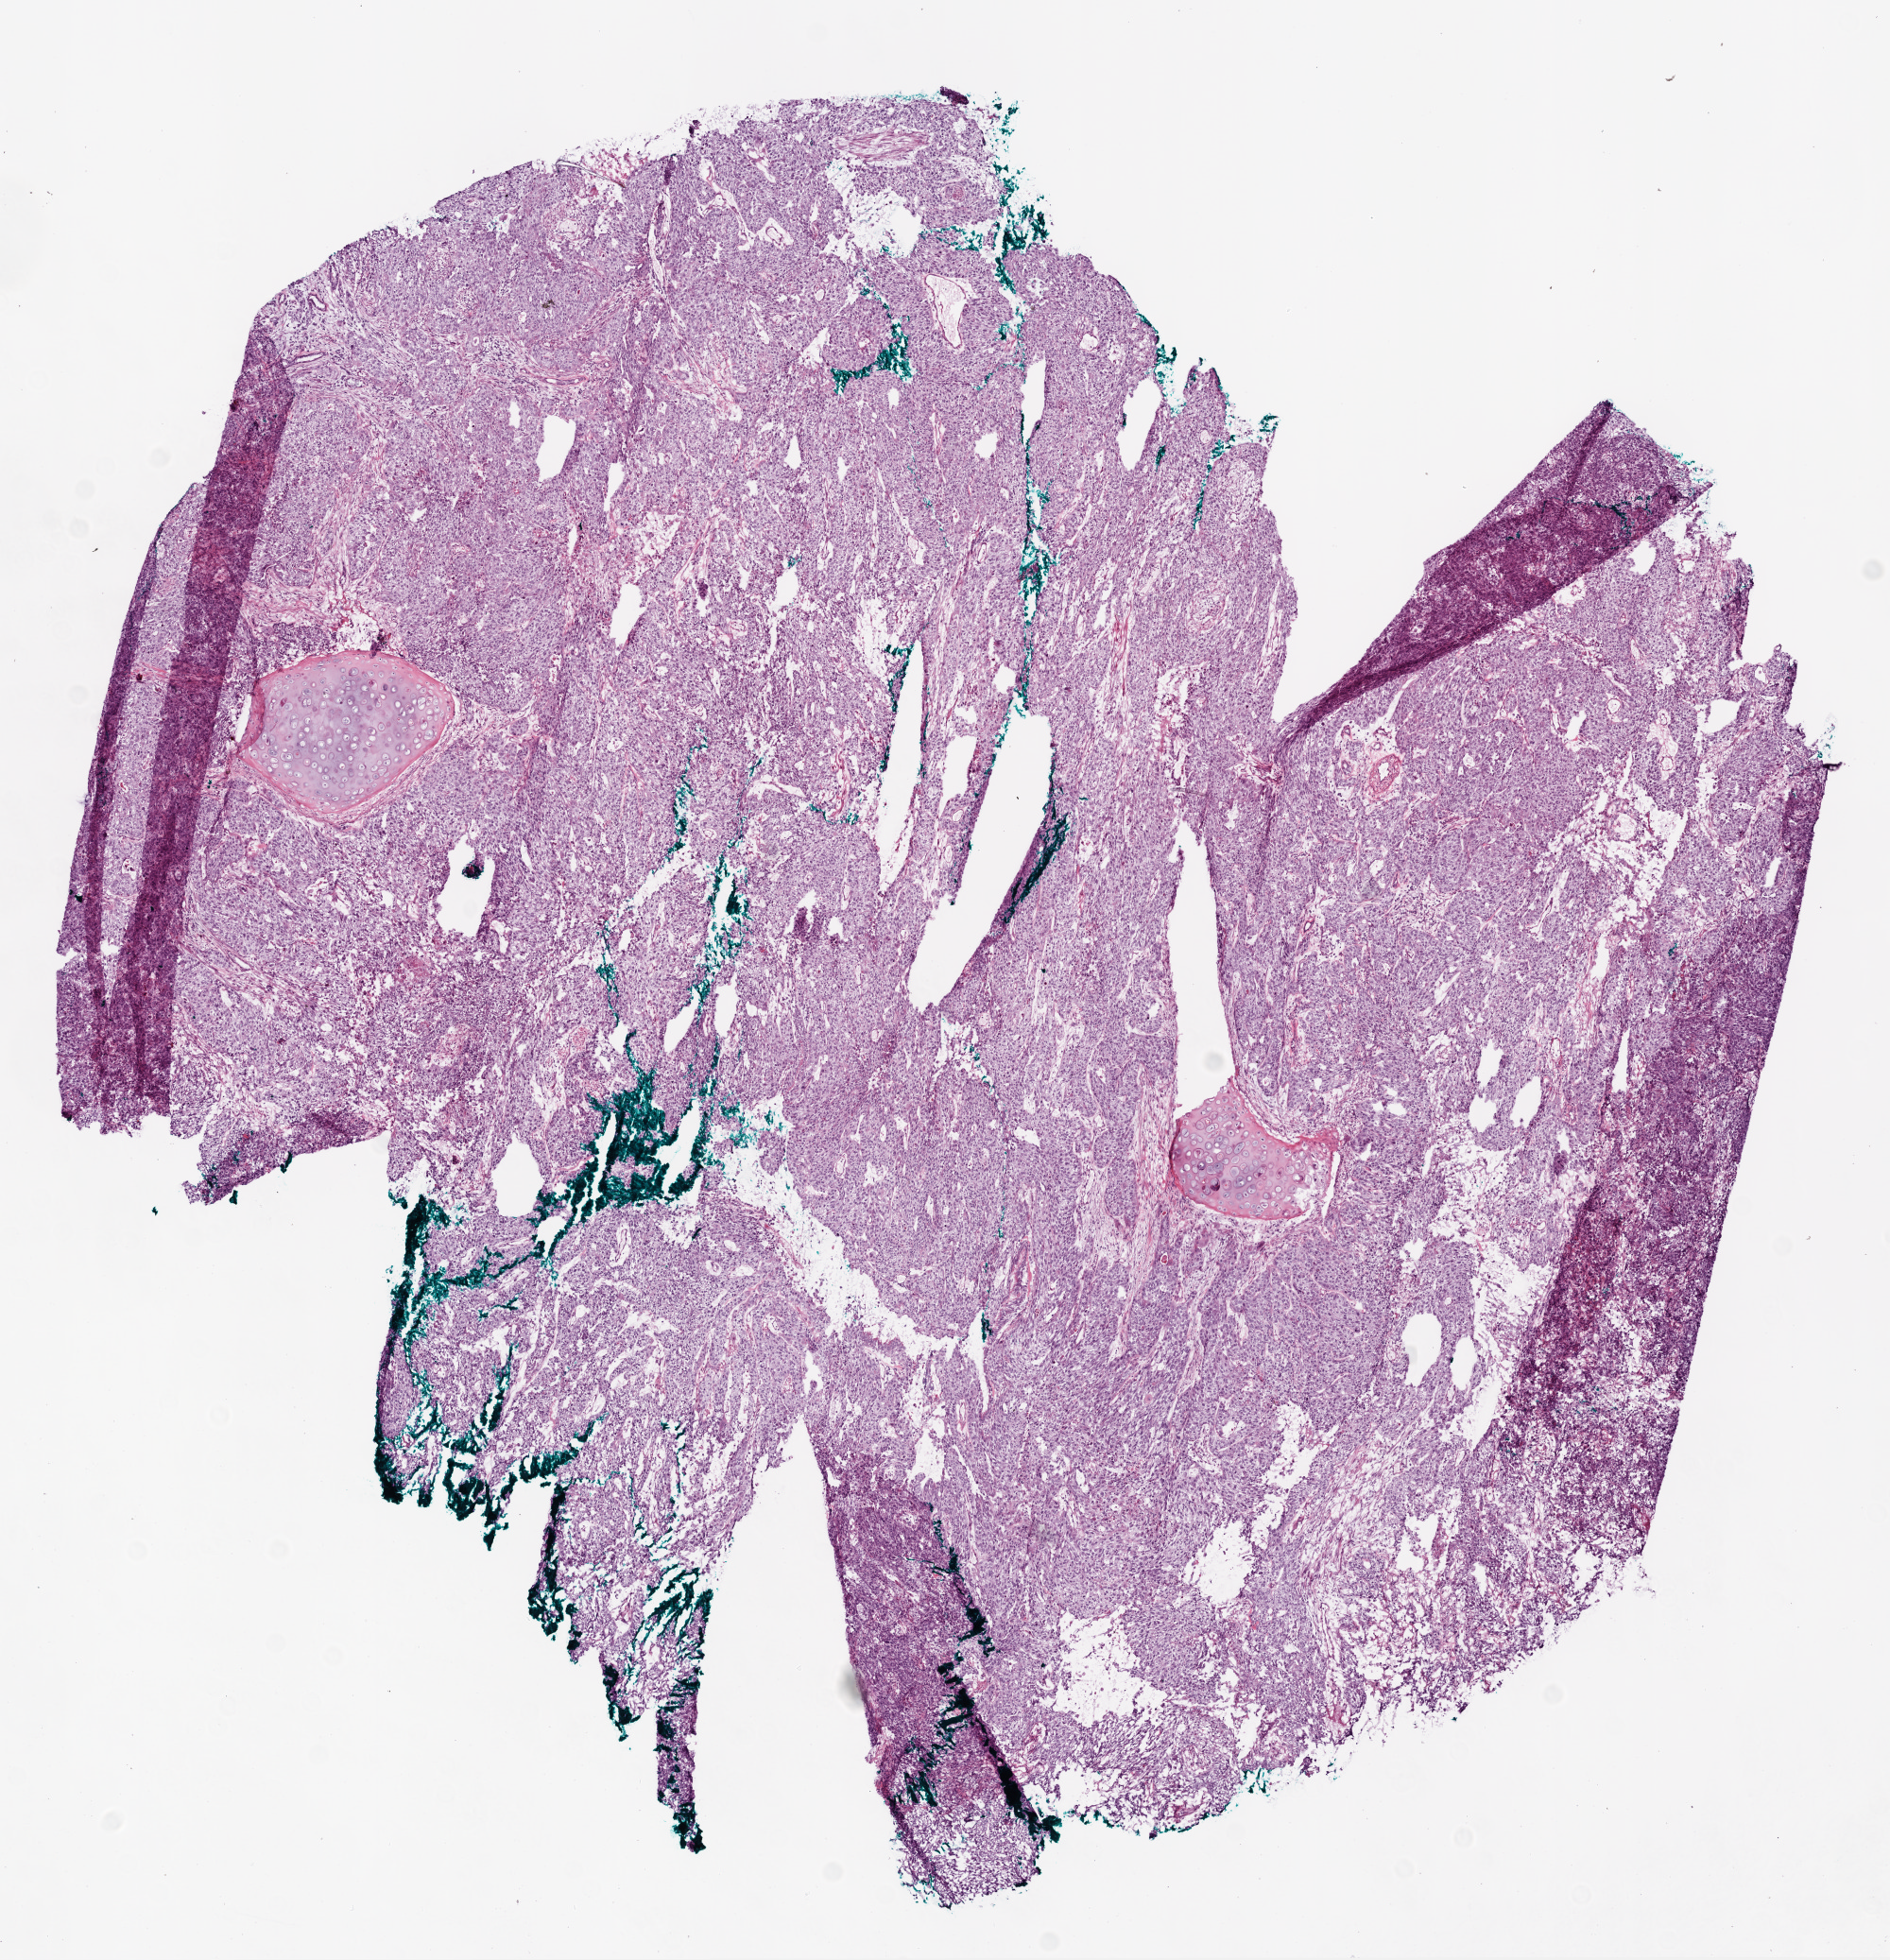
Whole-slide histology image, Hematoxylin and eosin (H&E) stained, whole scanned area (about 8.0 x 8.3 mm) shown as a low-resolution overview; frozen section; lung, primary tumour sample. Male, age 58 years at initial diagnosis. Slide review estimates, as recorded: tumour cells 89%, tumour nuclei 90%, normal cells 0%, stromal cells 10%, necrosis 1%.
AJCC pathologic stage: IB. Histologic diagnosis: Squamous cell carcinoma, NOS (lower lobe, lung). Laterality: right. TNM: T2 N0 M0.